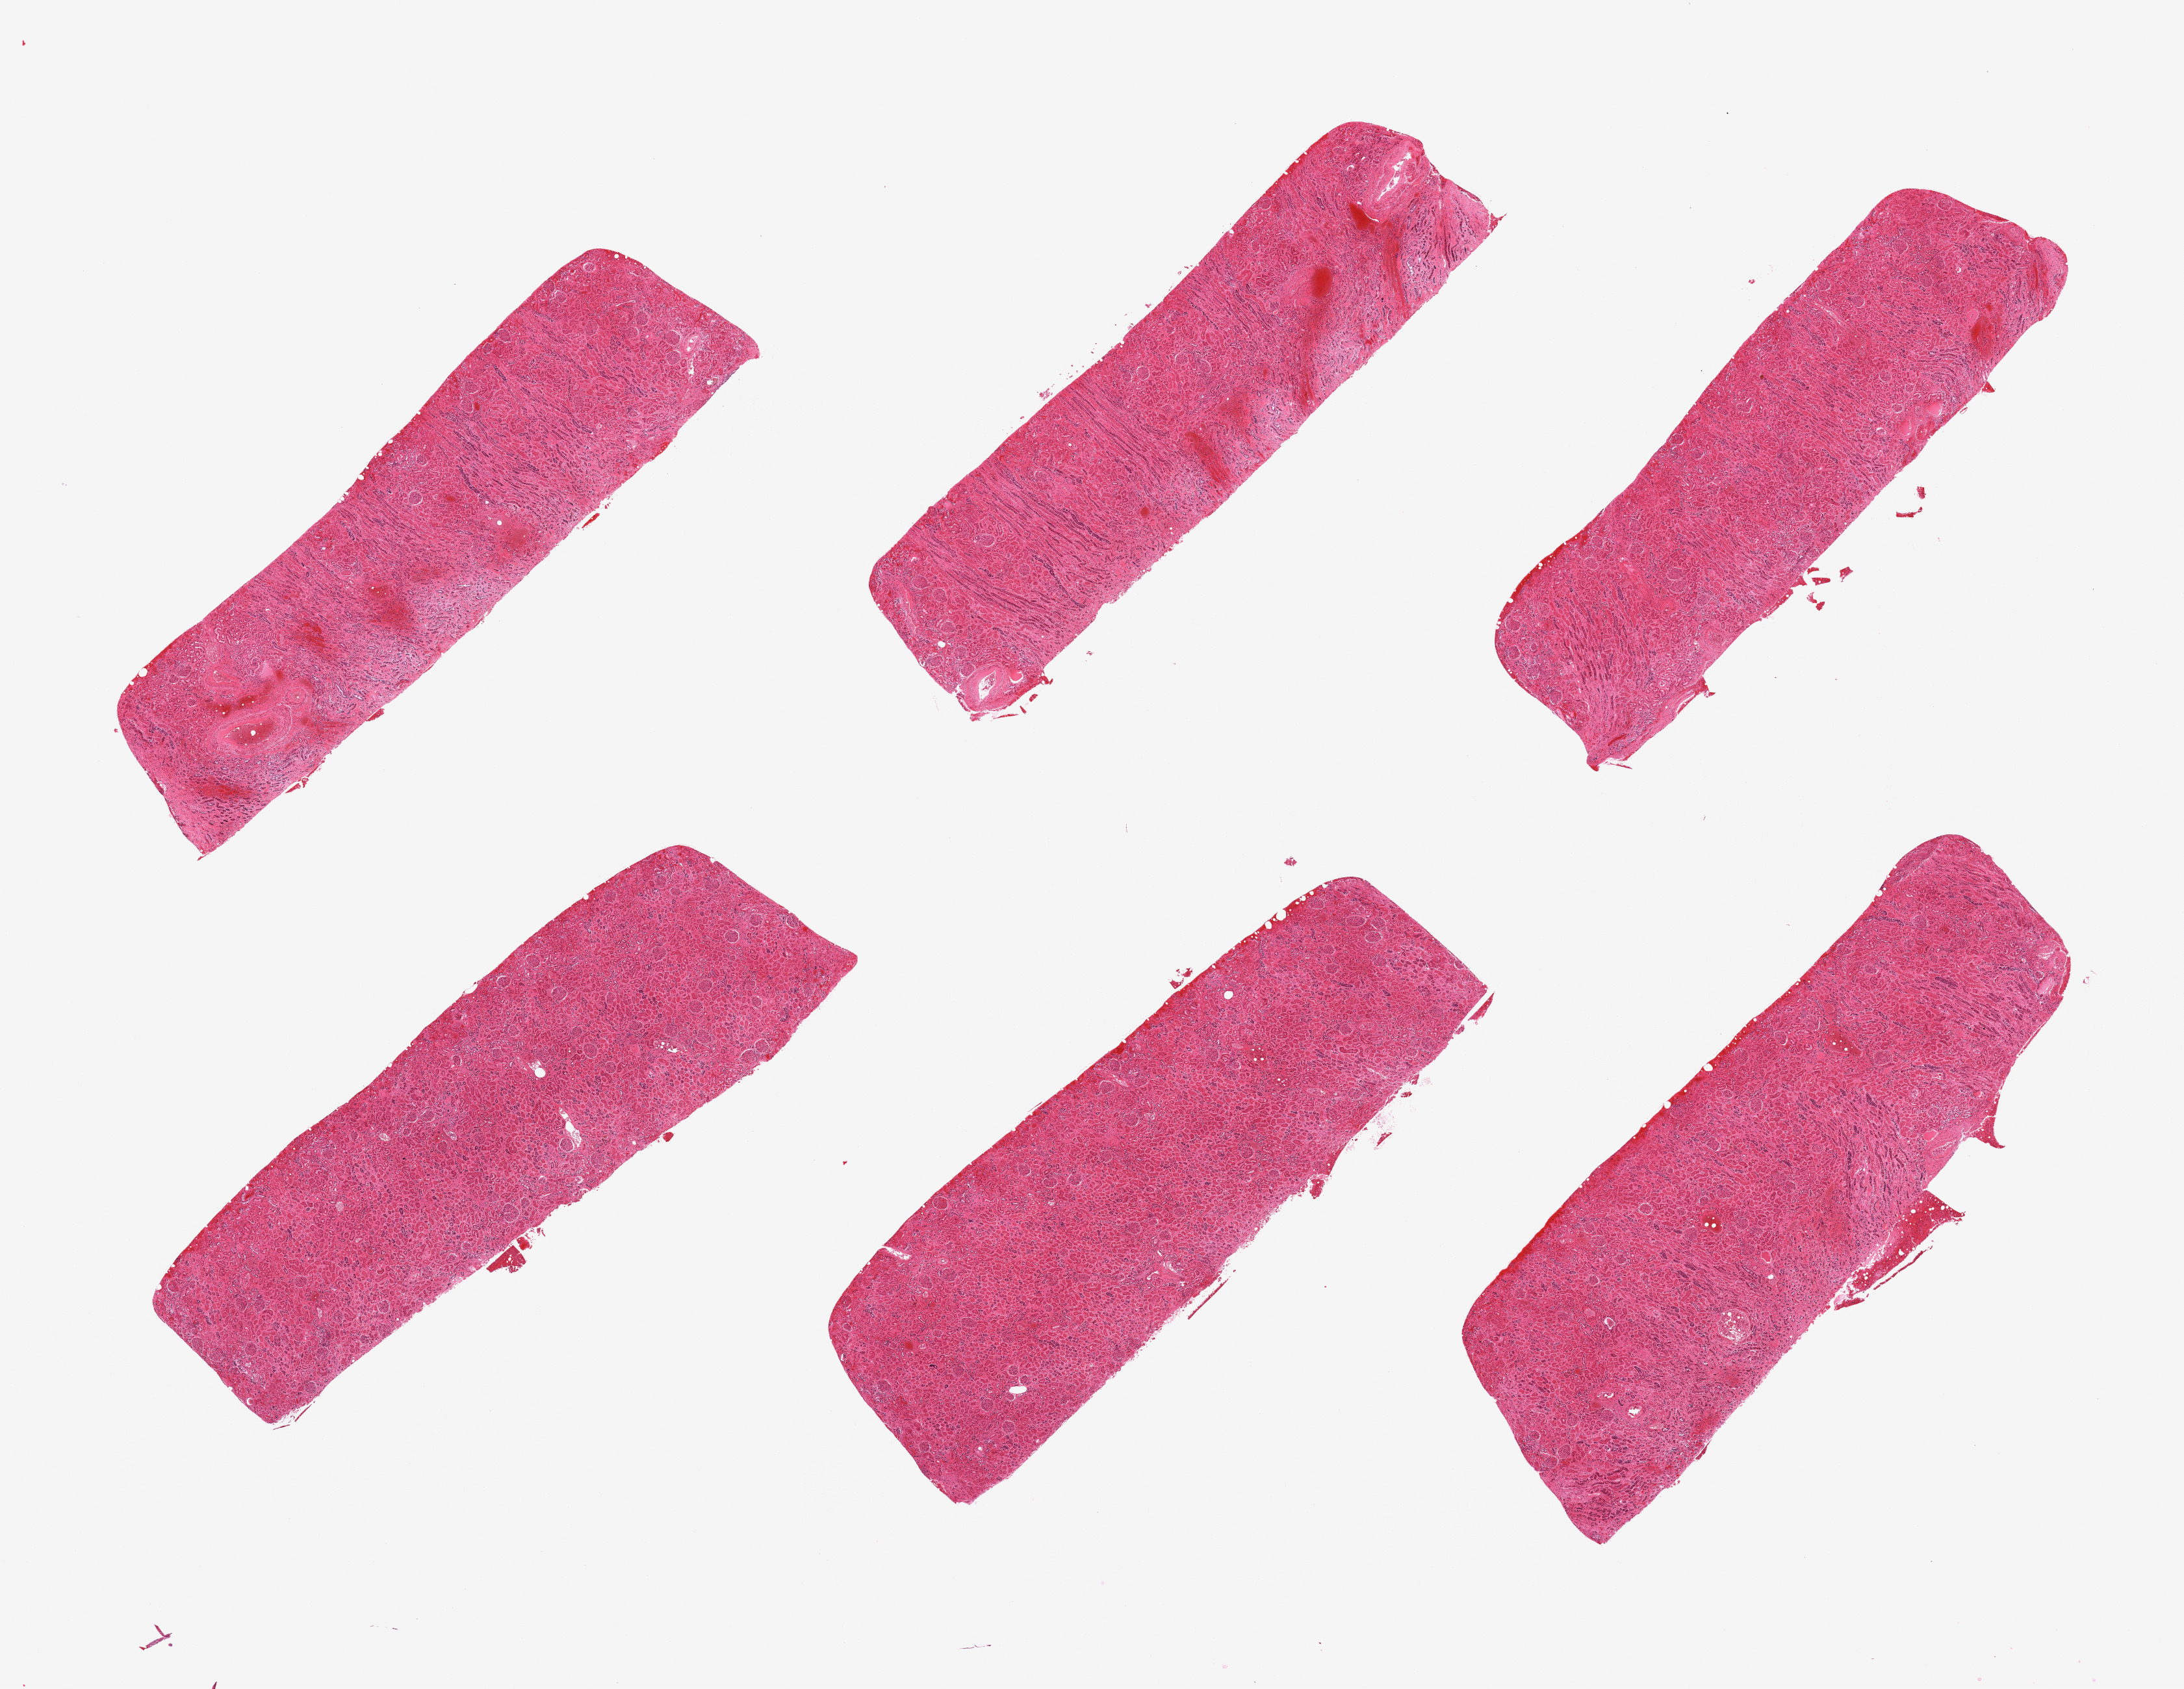
Haematoxylin and eosin whole-slide image, whole scanned area (about 26.6 x 20.6 mm) shown as a low-resolution overview. PAXgene-fixed, paraffin-embedded tissue. Sampled site (target tissue): renal cortex. Tissue donor sample. Male donor.
• review note (as recorded): 6 pieces, glomeruli present; all sections with advanced autolysis